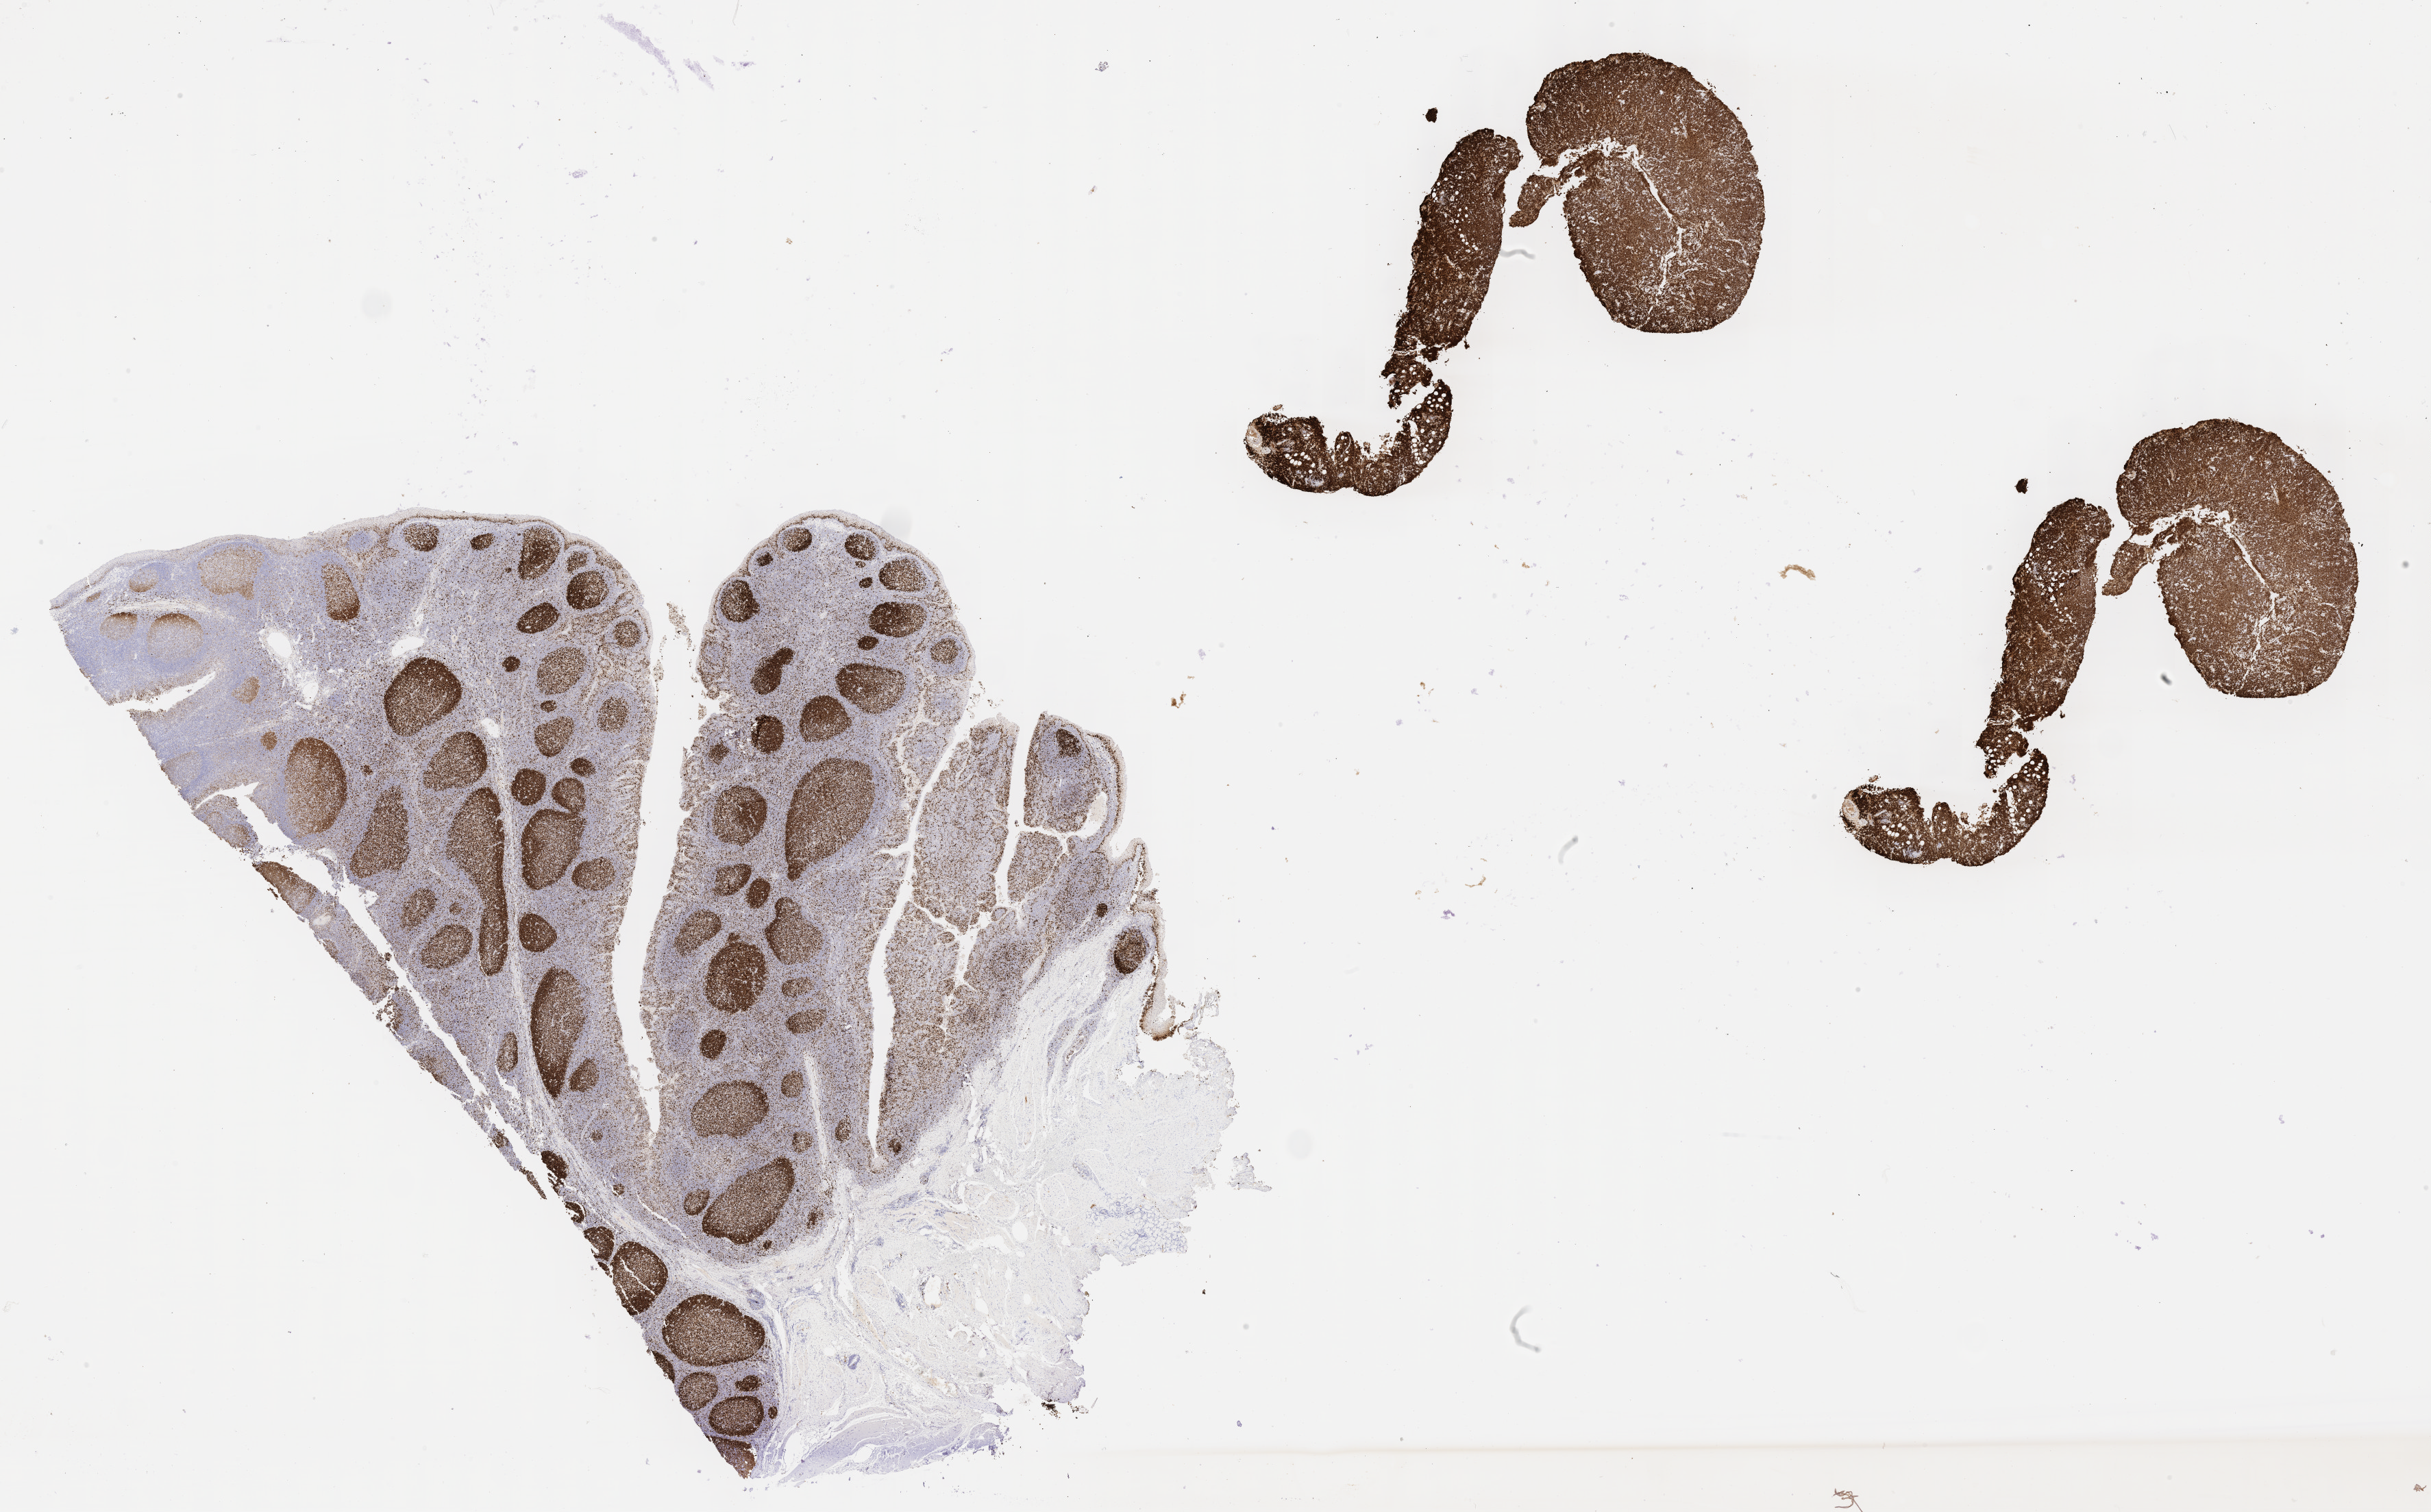
Immunohistochemistry (IHC) whole-slide image stained for Ki-67, shown as a low-resolution overview of the whole scanned area (about 28.7 x 17.8 mm). Specimen: tumor tissue. Anatomic site: head and neck. Patient: female, age 55 years.
Histologic diagnosis: Burkitt lymphoma, NOS.